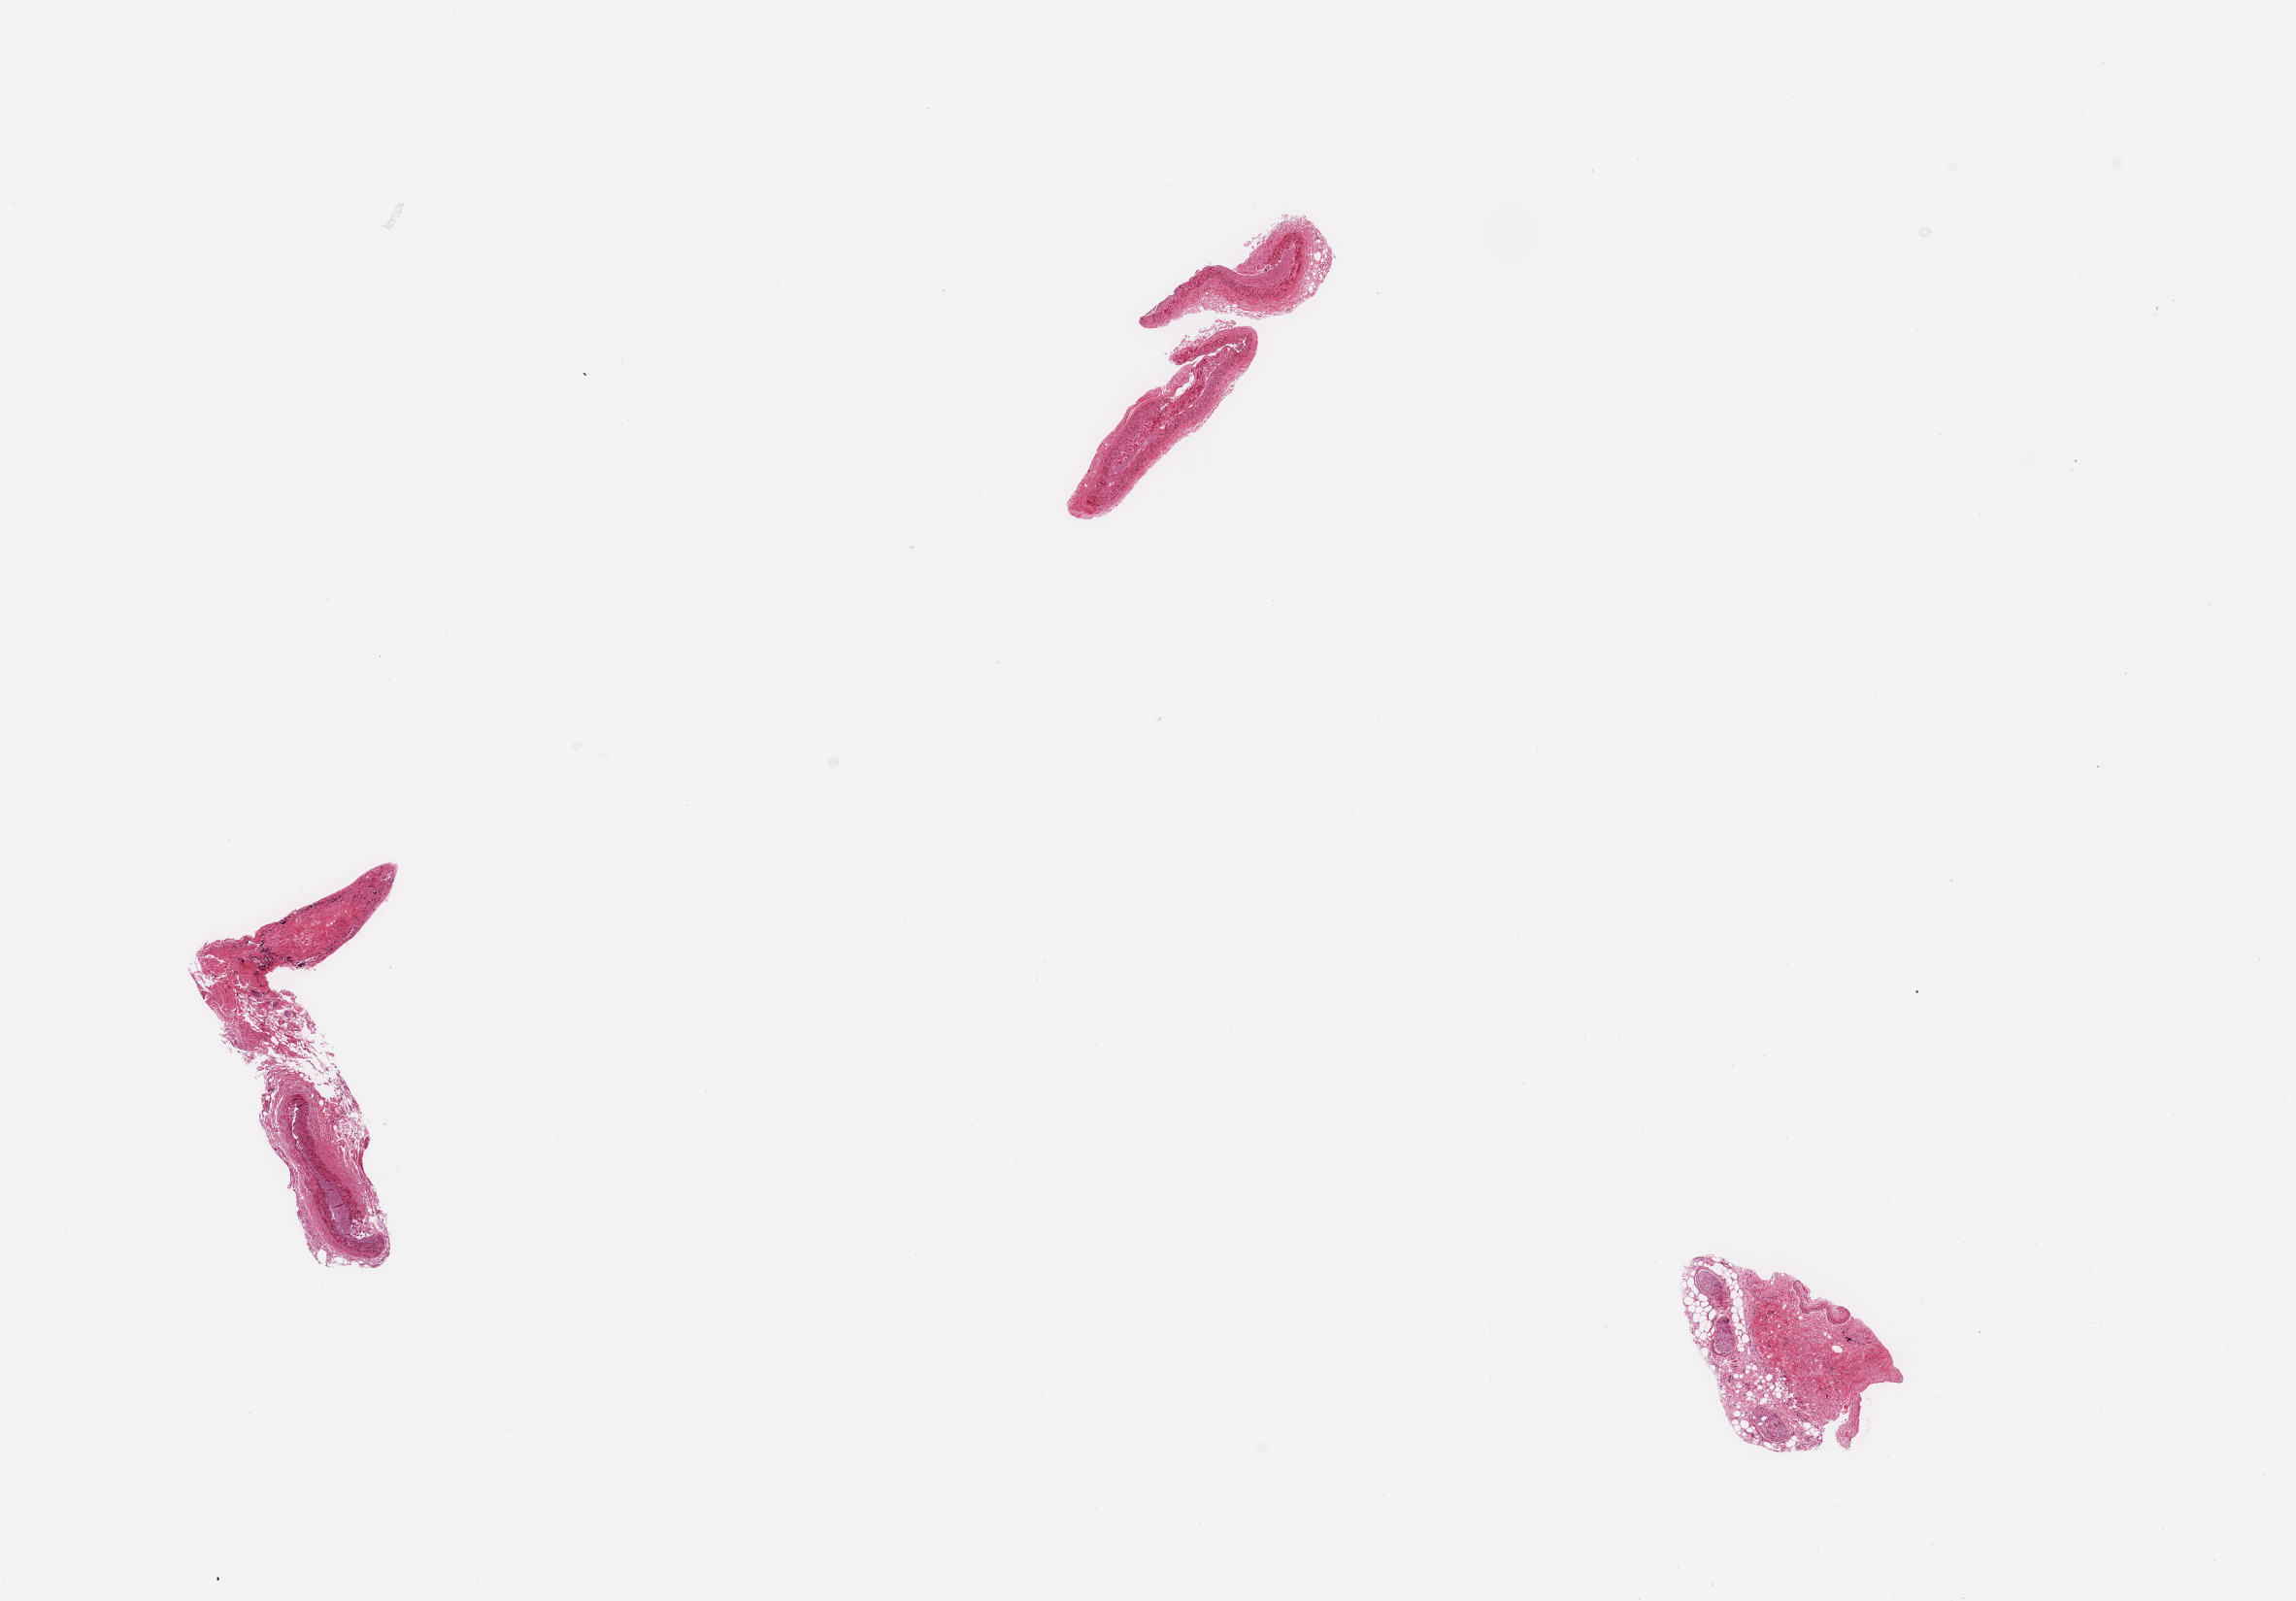
Digitized H&E-stained section — low-resolution overview of the scanned area, about 18.7 x 13.0 mm (from a 20x scan). PAXgene-fixed, paraffin-embedded tissue. Sampled site (target tissue): coronary artery. Donor tissue sample. Male donor.
Review note (as recorded): 3 pieces; 1 with small artery, 1 with small artery & 50% extraneous fibrous stroma; 1 with vein remnant & 90% fibrous & neural tissue.